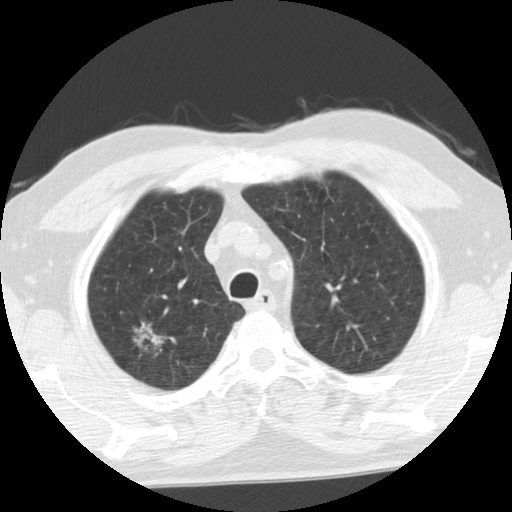
Axial slice from a low-dose chest CT screening exam; second annual screen; lung window (W 1500 / L -600 HU); 2.5 mm slice thickness; slice 91 of 116 in the series. Male participant, aged 68 years at enrolment. Former smoker at enrolment.
Expert-annotated lung lesion, bounding box [x1, y1, x2, y2] px = [129, 313, 167, 350]. Reader record for this screening exam (exam-level; its link to the box is not recorded): non-calcified nodule or mass ≥4 mm, right upper lobe, poorly defined margins, ground glass attenuation, pre-existing on the prior screen: yes; interval growth: yes. Later outcome: lung cancer diagnosed 88 days after this screen — adenocarcinoma, NOS, right upper lobe, moderately differentiated (G2), stage IA (AJCC 6th edition), 28 mm at pathology.